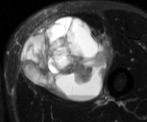
MRI of an extremity soft-tissue mass, one axial slice. Position 29 of 52 along the scan axis. T2-weighted fat-saturated. MR volume resampled by the dataset authors to the PET/CT grid (not the native acquisition matrix). 3.27 mm slice thickness. 147 × 122 image matrix. Male patient. From the clinical record (not read from this slice): histological type: pleiomorphic liposarcoma; grade: high; site of the primary tumour: left thigh.
Outlined on this slice (expert contour drawn on MRI and transferred to this co-registered scan by the dataset authors):
- gross tumour volume including surrounding oedema: bounding box (x1, y1, x2, y2) in pixels: (21, 15, 115, 100)
- gross tumour volume (mass): (21, 16, 111, 100)